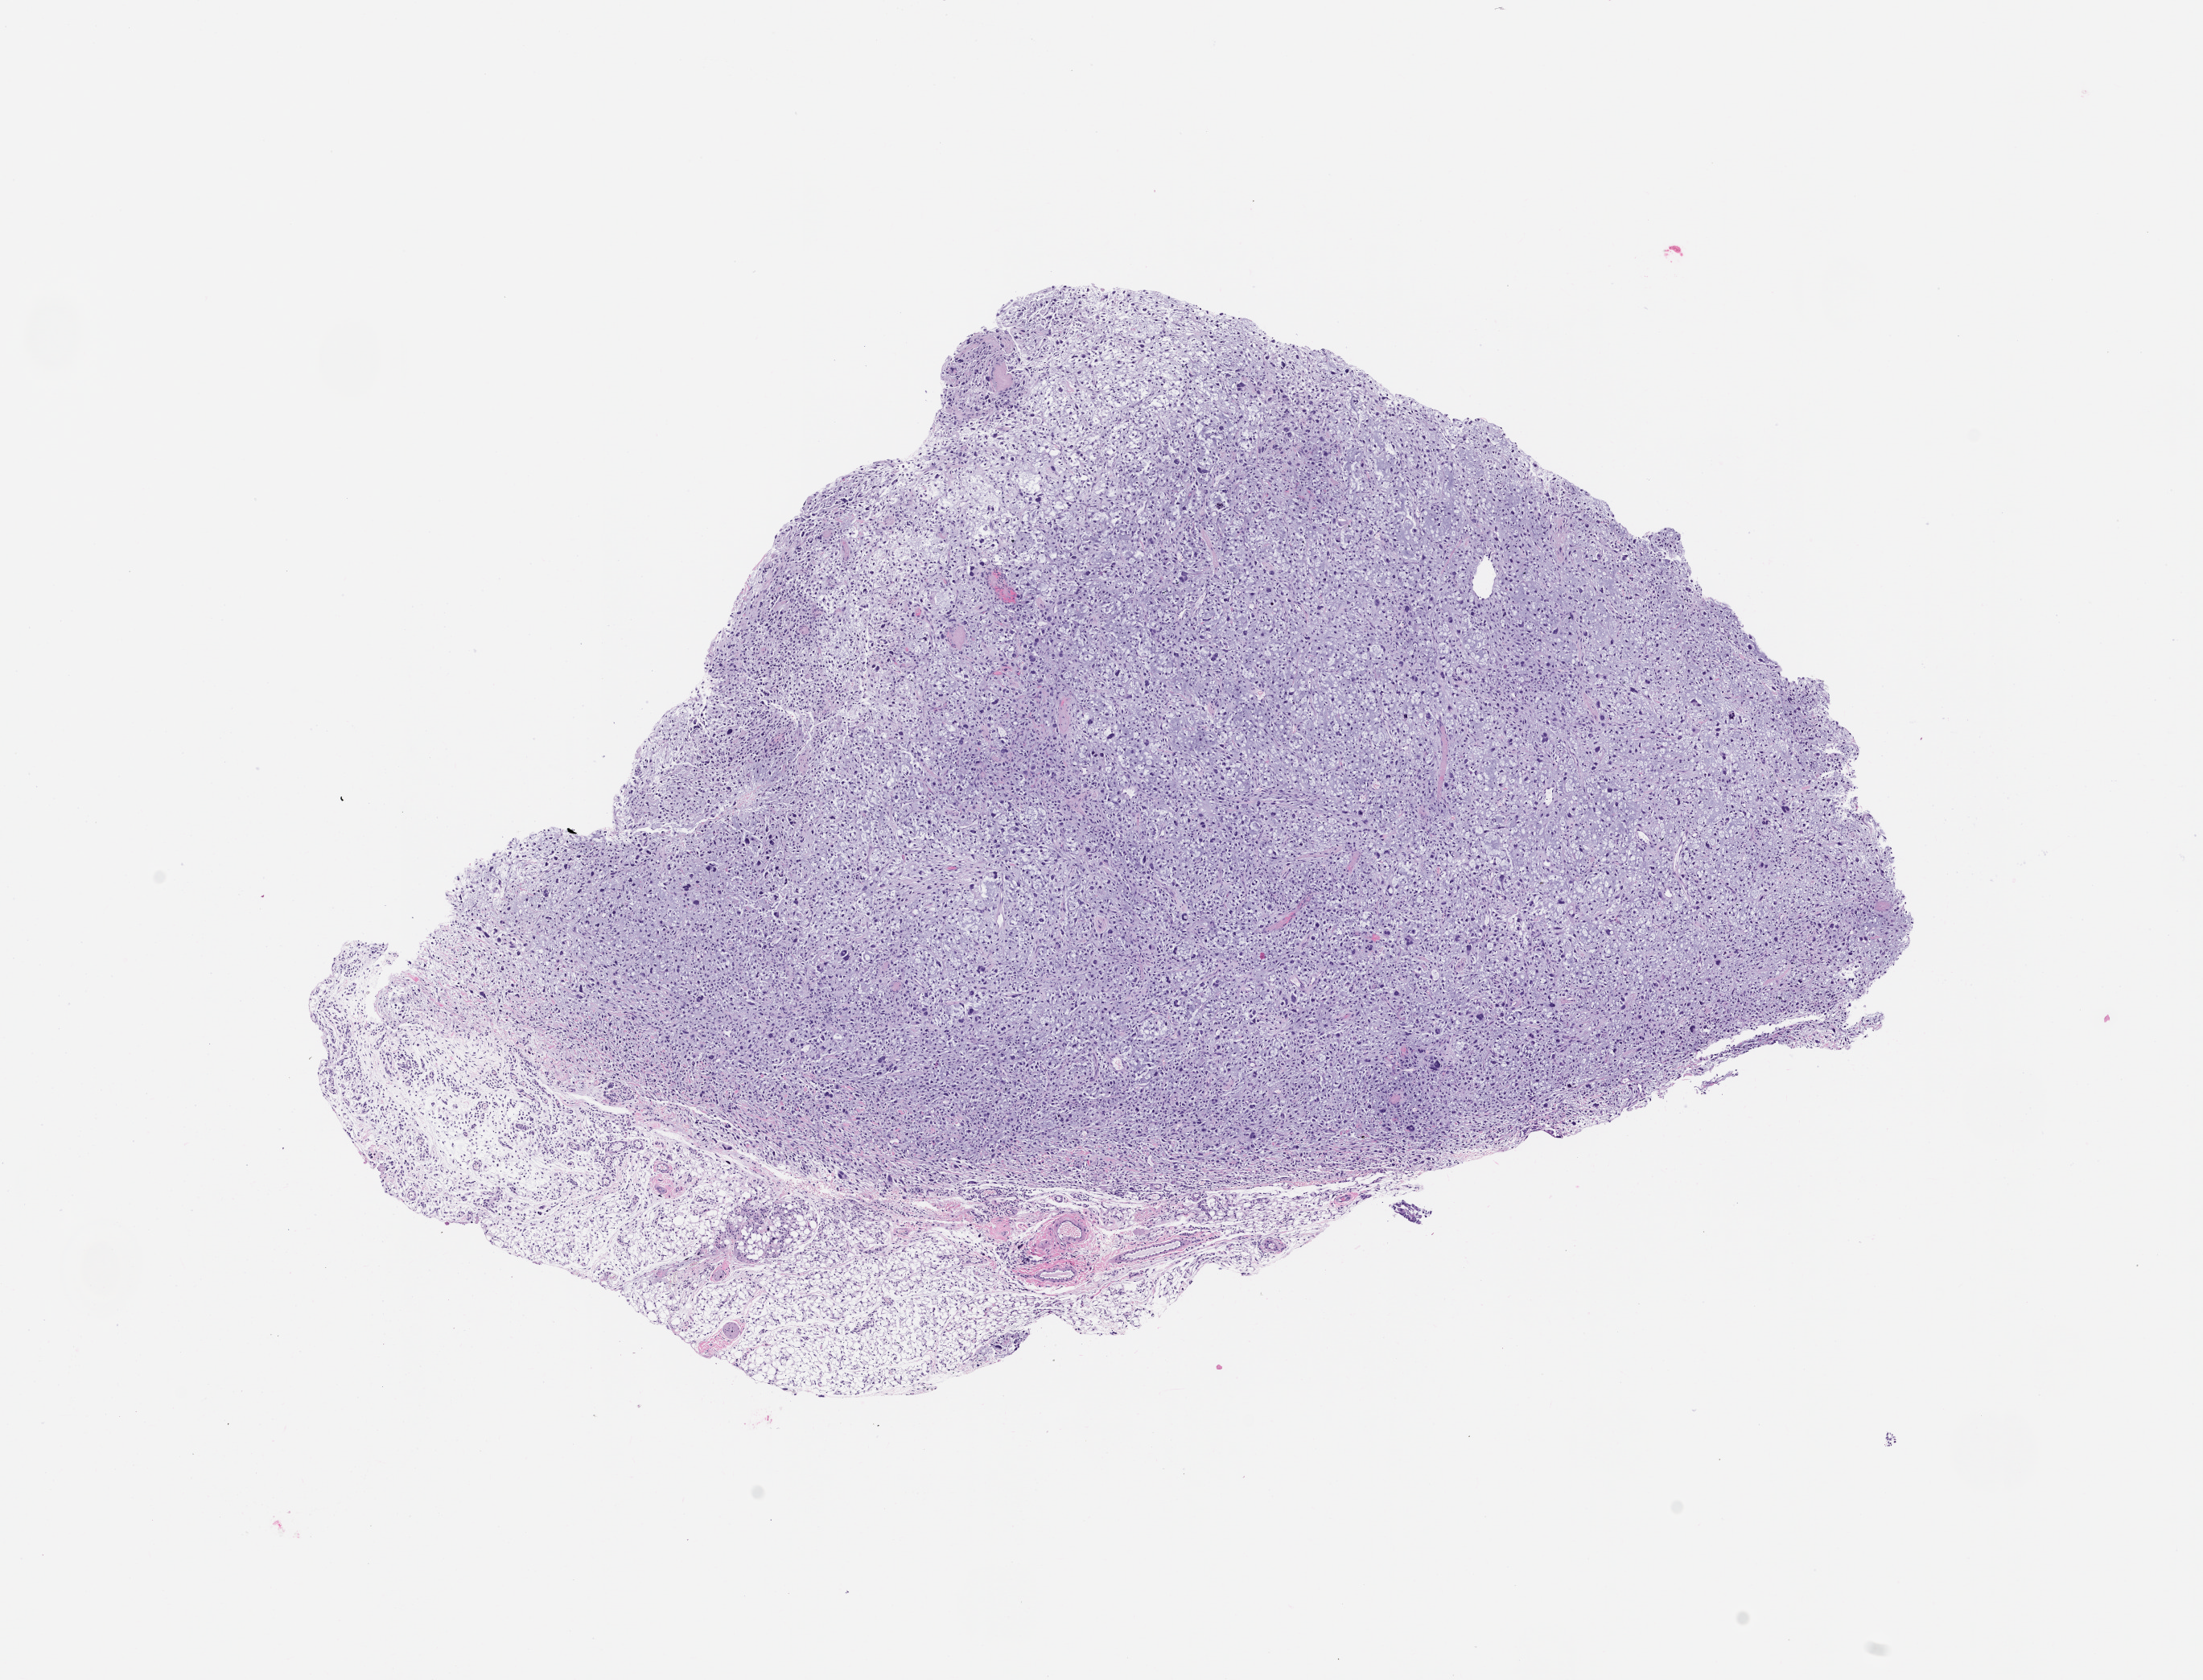
Whole-slide image, haematoxylin and eosin: patient-derived xenograft (human tumor grown in a mouse), passage 0 — a low-resolution overview of the entire scanned area, about 11.0 x 8.4 mm, formalin-fixed, paraffin-embedded (FFPE) tissue, tumor site category: musculoskeletal.
- originating patient diagnosis: Myxofibrosarcoma